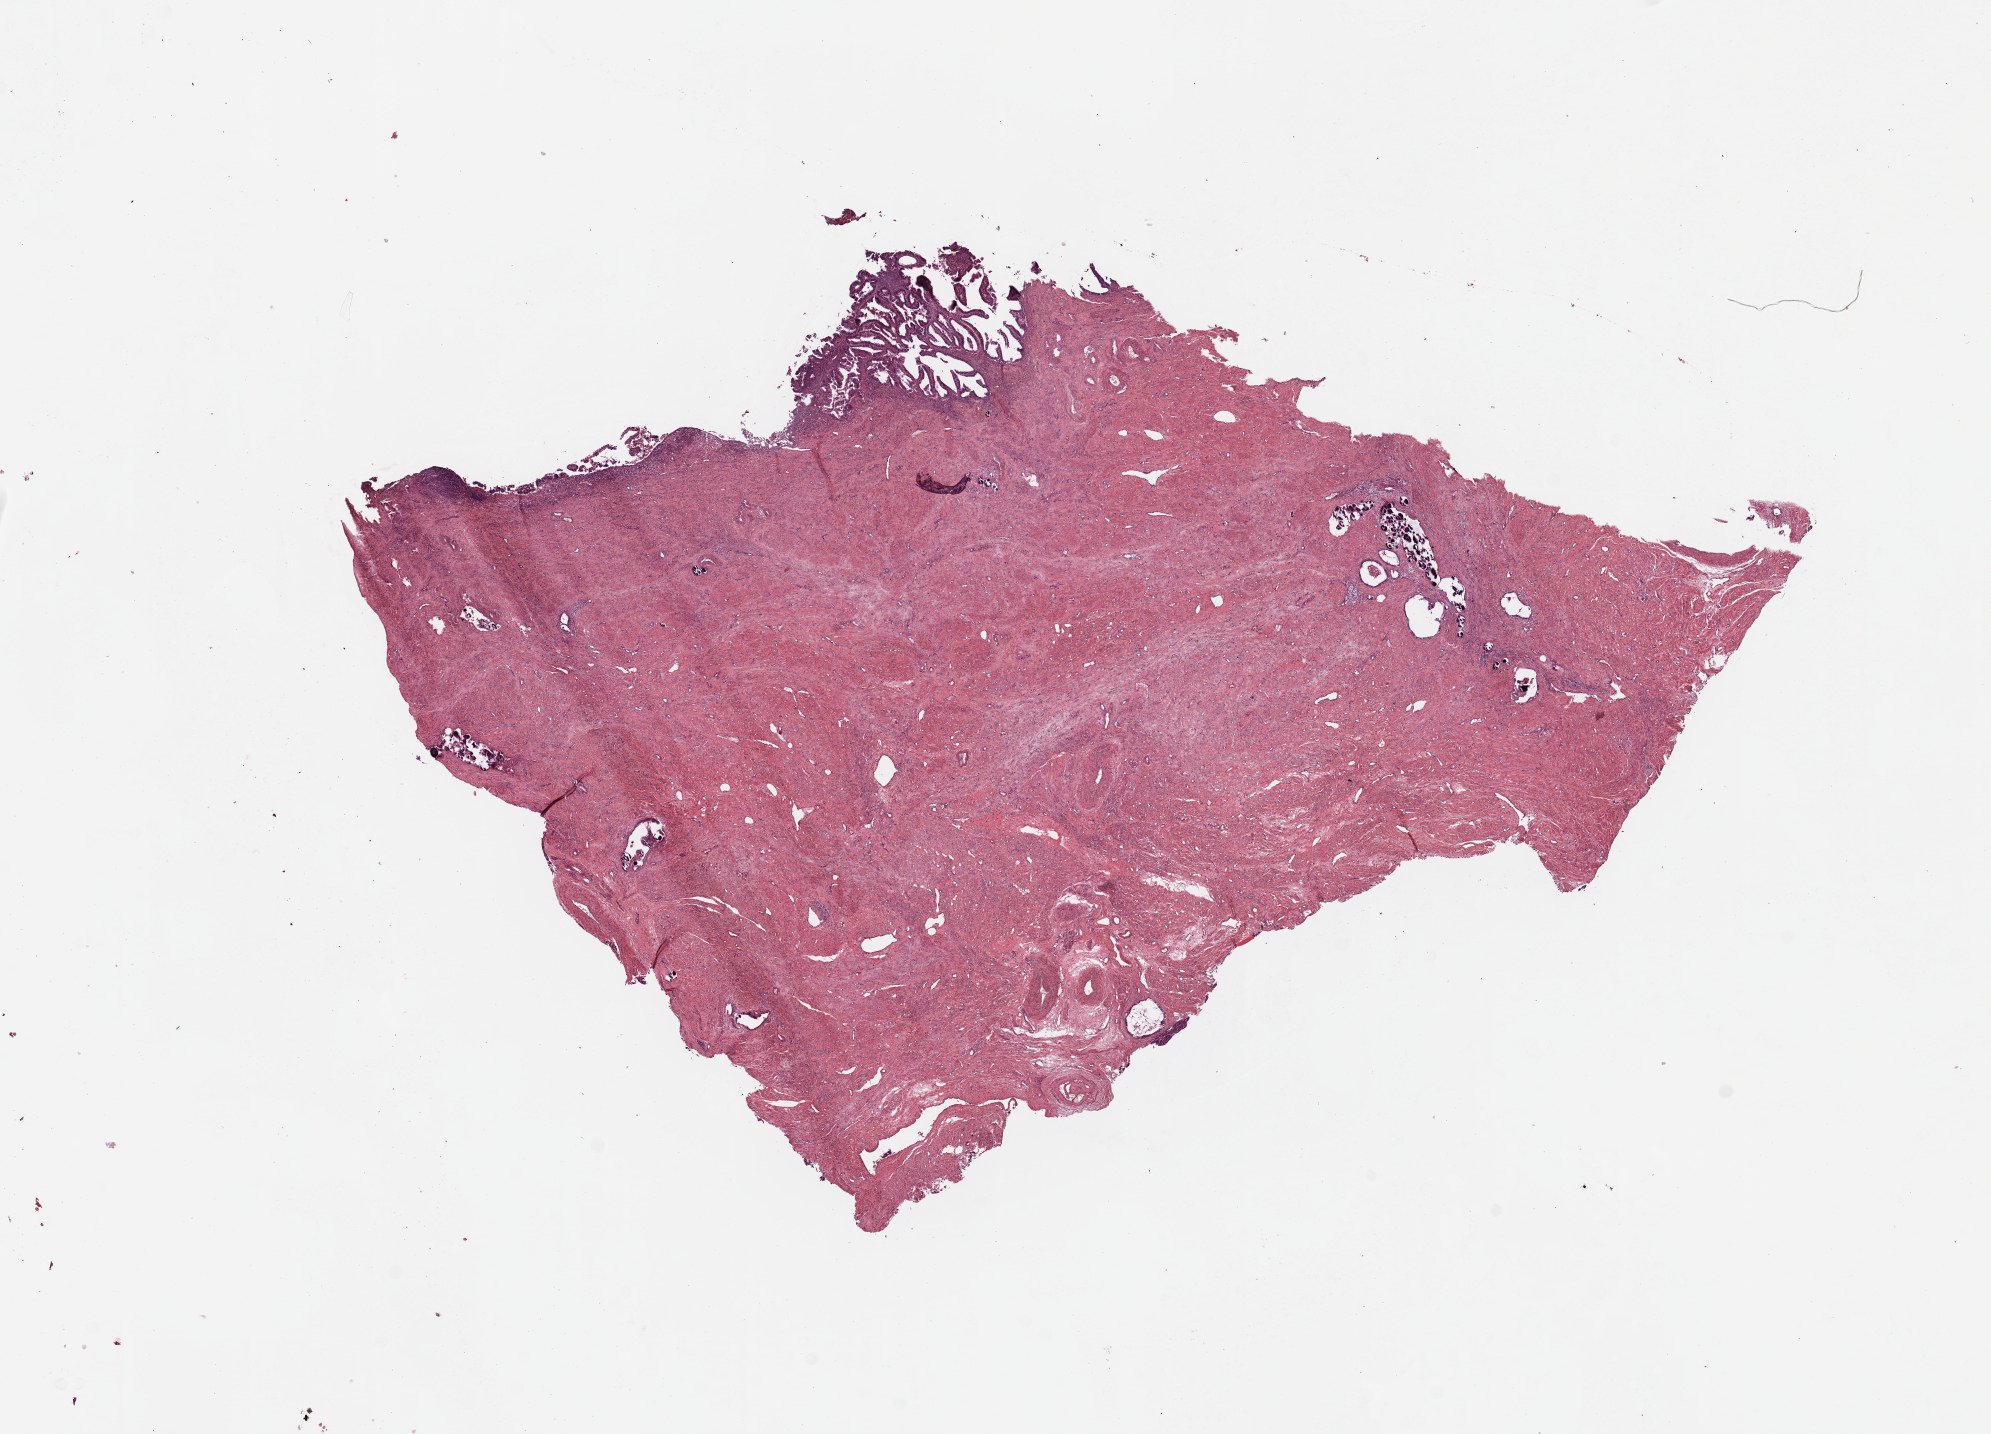
Digitized H&E-stained tissue section (whole slide) — whole scanned area (about 15.8 x 11.3 mm, acquisition: 20x scan) shown as a low-resolution overview. Tumour tissue sample, sampled site: uterus. 70-year-old female patient. Histologic grade: G3 (poorly differentiated). Pathologist review of this section (percent, as recorded): tumour nuclei 10%, necrosis 0%.
• histologic diagnosis: Endometrioid adenocarcinoma, NOS
• AJCC pathologic stage: I